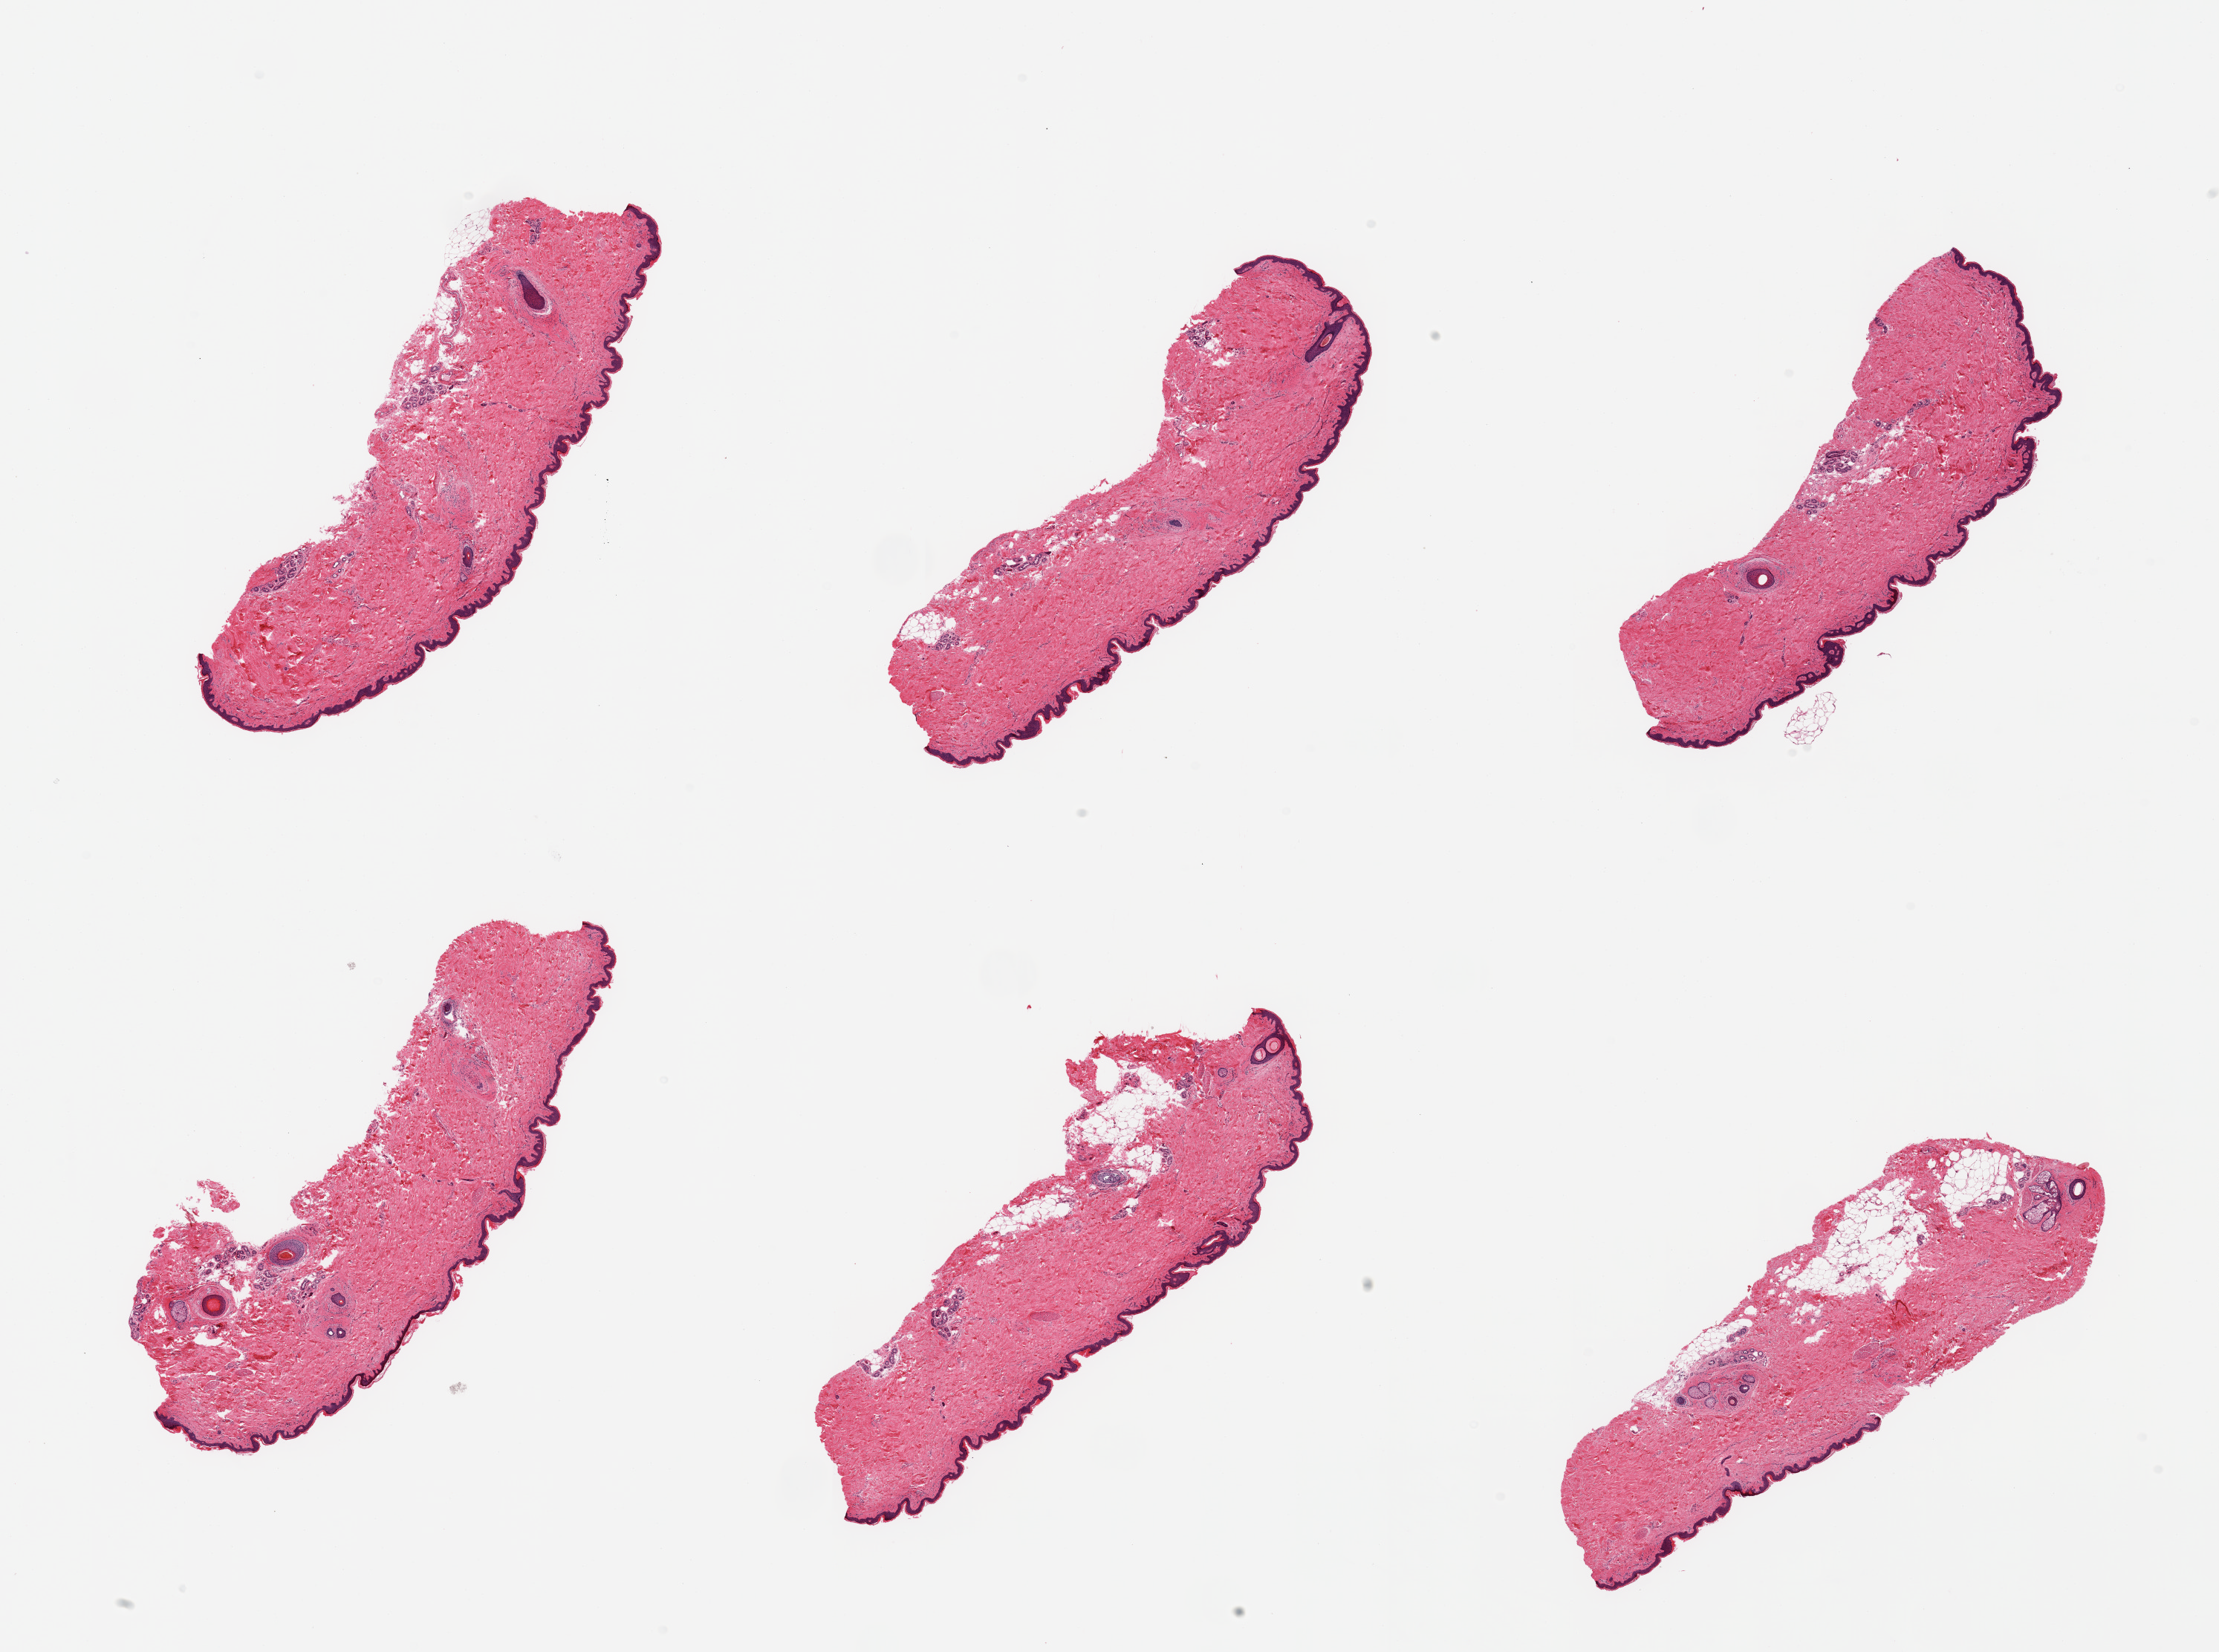
Digitized hematoxylin and eosin (H&E)-stained section, a low-resolution overview of the entire scanned area, about 23.6 x 17.6 mm (acquisition: 20x scan). PAXgene-fixed paraffin-embedded (PFPE) section. Sampled site (target tissue): skin of suprapubic region. Donor tissue sample. Donor sex: female.
Review note (as recorded): 6 pieces; well trimmed; 10 & 20% dermal fat in 2 pieces.